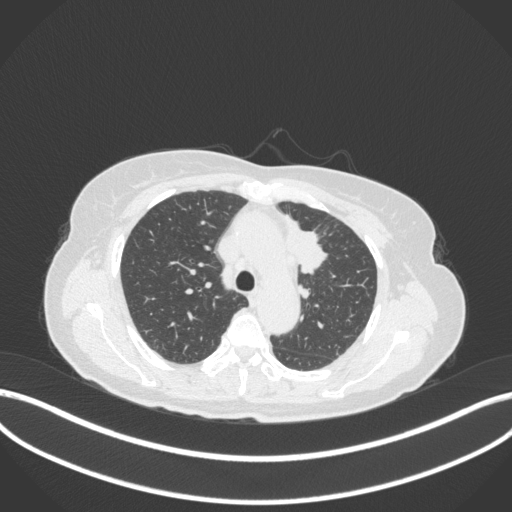
Chest CT, one axial slice; slice 238 of 368 in the series (ordered by position); reconstruction kernel B31f; lung window (W 1500 / L -600 HU); 1 mm slice thickness; 512 × 512 image matrix, field of view 400 × 400 mm. Patient: female, 65 years. Case-level facts recorded for this patient, not image findings: clinical TNM (as recorded): T2a N0 M0; histopathological grade: G2-3.
Annotated regions visible in this slice (rectangle marked by the reading radiologist):
- lung tumour (recorded histology: adenocarcinoma): bounding box (x1, y1, x2, y2) in pixels: (281, 214, 330, 278)